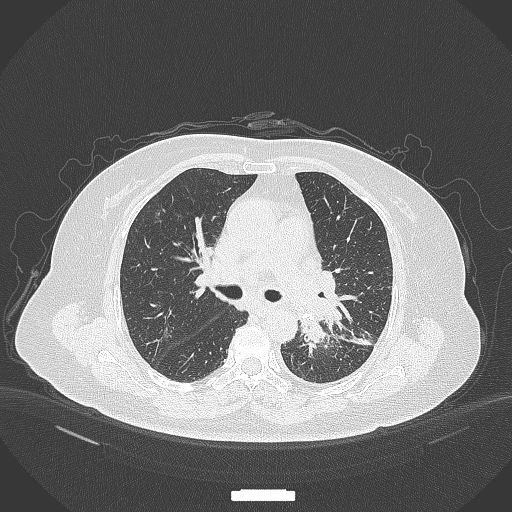
Chest CT, one axial slice. Slice 215 of 322 in the series (ordered by position). Reconstruction kernel B70f. Lung window (W 1500 / L -600 HU). 512 × 512 image matrix. Female patient, age 69 years. Case-level facts recorded for this patient, not image findings: clinical TNM (as recorded): T2b N3 M1.
Annotated regions visible in this slice (bounding box drawn by a radiologist):
- lung tumour (recorded histology: adenocarcinoma): bounding box <294,313,332,354> (left, top, right, bottom; pixels)